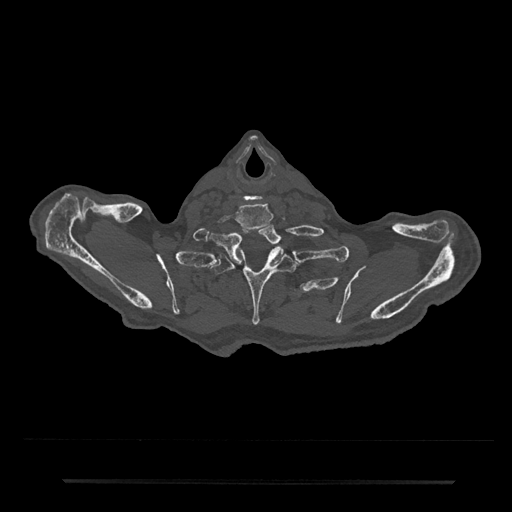
CT including the spine, one axial slice; slice 709 of 797 in the series (ordered by position); 120 kVp; bone window (W 1800 / L 400 HU); 0.5 mm slice thickness; 512 × 512 image matrix, field of view 427 × 427 mm. Male patient, age 74 years. From the clinical record (not read from this slice): primary cancer: prostate.
Annotated regions visible in this slice (semi-automatically segmented with operator editing):
- T1 vertebra: bounding box (x1, y1, x2, y2) in pixels: (213, 223, 284, 265)
- T2 vertebra: (210, 248, 303, 326)
- T3 vertebra: (293, 289, 300, 296)